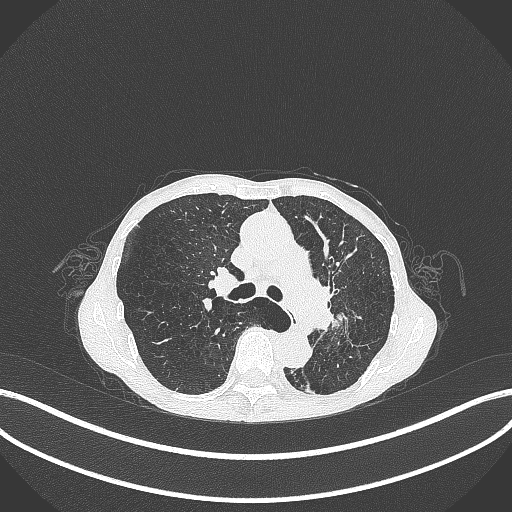
Chest CT, one axial slice; position 178 of 347 along the scan axis; lung window (W 1500 / L -600 HU); 512 × 512 image matrix, field of view 400 × 400 mm. Female patient, age 70 years. Case-level facts recorded for this patient, not image findings: clinical TNM (as recorded): T3 N0 M0; histopathological grade: G3.
Outlined on this slice (rectangle marked by the reading radiologist):
- lung tumour (recorded histology: small cell carcinoma): bounding box (x1, y1, x2, y2) in pixels: (326, 303, 351, 337)